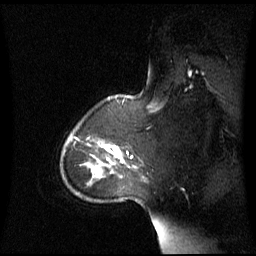
Breast MRI (dynamic contrast-enhanced), one sagittal slice; dynamic contrast-enhanced series, image 2 of 3 at this slice position (ordered by acquisition); 1.5 T; TE 4.2 ms, TR 8.4 ms; 2.8 mm slice thickness; 256 × 256 image matrix, field of view 270 × 270 mm. Female patient, age 43 years. Case-level facts recorded for this patient, not image findings: setting: breast cancer imaged before/during neoadjuvant chemotherapy; receptor status: triple-negative.
Structures marked on this image (semi-automatically segmented with operator editing):
- analysis volume of interest (the breast-tissue region the enhancement analysis was run in; not a lesion): bounding box <62,124,137,180> (left, top, right, bottom; pixels)
- tumour enhancement mask (voxels above the 70 % enhancement threshold inside the analysis volume of interest): <95,144,133,166>